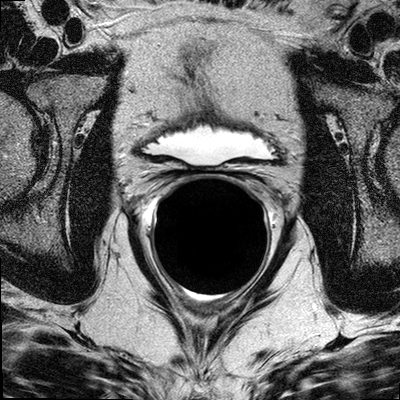
MRI of the prostatic bed after radical prostatectomy; 3 images, each a single mid-volume slice chosen by position (not for content). Treatment context recorded for this patient: Post-op.
Image 1: axial T2-weighted image, series "T2W_TSE_AX", slice 17 of 32, 3 mm slice thickness.
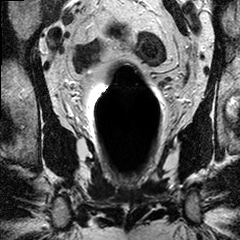
Image 2: T2-weighted coronal slice, series "T2W_TSE_COR", slice 13 of 24, 3 mm slice thickness.
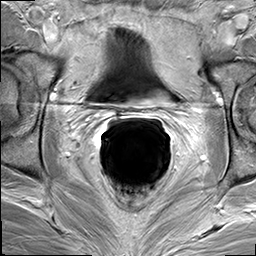
Image 3: axial dynamic contrast-enhanced (DCE) T1-weighted image, series "dyn_THRIVE", slice 19 of 36, dynamic phase 5 of 9.
Report of this MRI examination:
FINDINGS: Regular findings seen within the surgical bed. Multiple surgical clips within the prostatic bed and around the anastomosis. Regular appearance of the anastomosis. No definite masses seen within the prostatic bed. No foci of suspicious enhancement in and around the prostatic bed. Unremarkable urinary bladder. No remnant seminal vesicles present. No suspiciously enlarged obturator and iliac lymph nodes. Several small 4-7 mm lymph nodes seen along the iliac vessels bilateral. The visualized osseous structures without evidence of involvement. Multiplanar reconstructions, subtraction images, and CAD analysis of the dynamic series for assessment of the kinetic information facilitated the interpretation of the exam. IMPRESSION: No evidence of local recurrence or pelvic lymph adenopathy. No suspicious mass. No suspiciously enlarged obturator or iliac lymph nodes. (Several up to 7 mm lymph nodes along the iliac vessels bilateral are non-specific). Normal appearance of the prostatic bed and anastomosis

Pathology / management note recorded for this patient (as recorded; not read from these images):
No specimen. initially diagnosed in with Gleason score 3+4=7 prostate adenocarcinoma,.treated with a robotic assisted radical prostatectomy and pelvic lymph node dissection 3 yrs ago. This revealed GS 3+4=7 moderately differentiated prostate adenocarcinoma, 0/2 LNs positive. There was no extracapsular extension or seminal vesicle invasion, however multiple margins were positive. It was a pT2cN0. His PSA had been 0.1 since that time. PSA on that date had increased to 0.2, up from 0.1. Repeat recent PSA was 0.3.